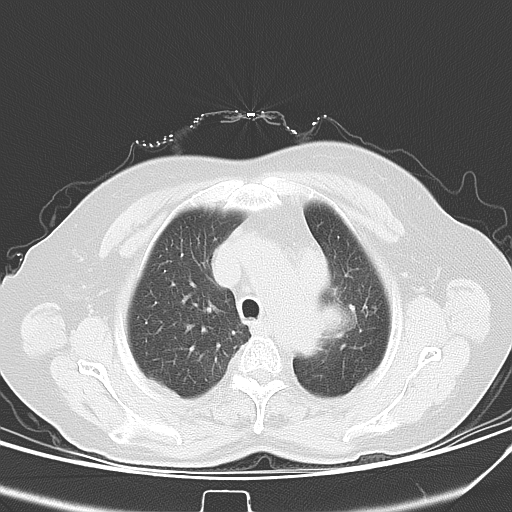
Chest CT, one axial slice; position 33 of 40 along the scan axis; 120 kVp; lung window (W 1500 / L -600 HU); 512 × 512 image matrix, field of view 331 × 331 mm. Female patient, age 59 years. Case-level facts recorded for this patient, not image findings: clinical TNM (as recorded): T3 N1 M0; histopathological grade: G3.
Structures marked on this image (bounding box drawn by a radiologist):
- lung tumour (recorded histology: small cell carcinoma): bounding box [x1, y1, x2, y2] px = [320, 296, 354, 344]